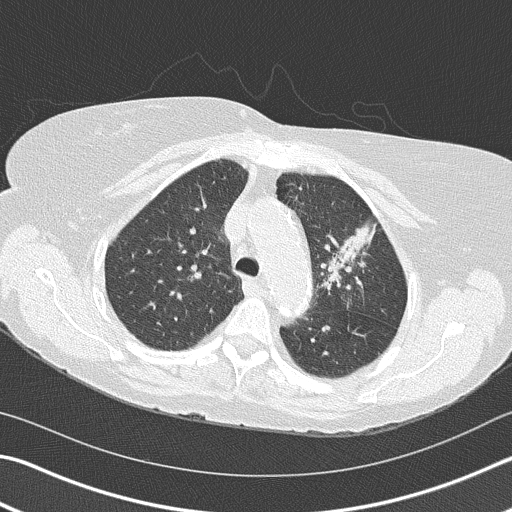
Axial slice from a low-dose chest CT screening exam, second annual screen, lung window (W 1500 / L -600 HU), 2 mm slice thickness. Female, age 68 years at enrolment.
• Expert-annotated lung lesion, bounding box [x1, y1, x2, y2] px = [293, 204, 388, 313].
• Screening reader's record for this exam (one nodule recorded; not confirmed to be the boxed lesion): non-calcified nodule or mass ≥4 mm, left upper lobe, 4 × 2 mm, spiculated (stellate) margins, soft tissue attenuation, pre-existing on the prior screen: yes; interval growth: yes.
• Later outcome: lung cancer diagnosed 392 days after this screen (after the third annual screen) — adenocarcinoma, NOS, left upper lobe, poorly differentiated (G3), stage IB (AJCC 6th edition), 50 mm at pathology.